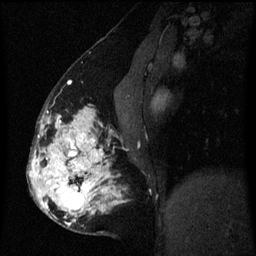
Breast MRI (dynamic contrast-enhanced), one sagittal slice. Position 28 of 60 along the scan axis. Dynamic contrast-enhanced series, image 2 of 3 at this slice position (ordered by acquisition). 1.5 T. TE 4.2 ms, TR 8 ms. 2 mm slice thickness. 256 × 256 image matrix, field of view 190 × 190 mm. Female patient, age 50 years.
Structures marked on this image (semi-automatic segmentation, software-assisted and operator-edited):
- analysis volume of interest (the breast-tissue region the enhancement analysis was run in; not a lesion): box from (x=32, y=107) to (x=123, y=232) px
- tumour enhancement mask (voxels above the 70 % enhancement threshold inside the analysis volume of interest): (x=32, y=107)–(x=123, y=226)